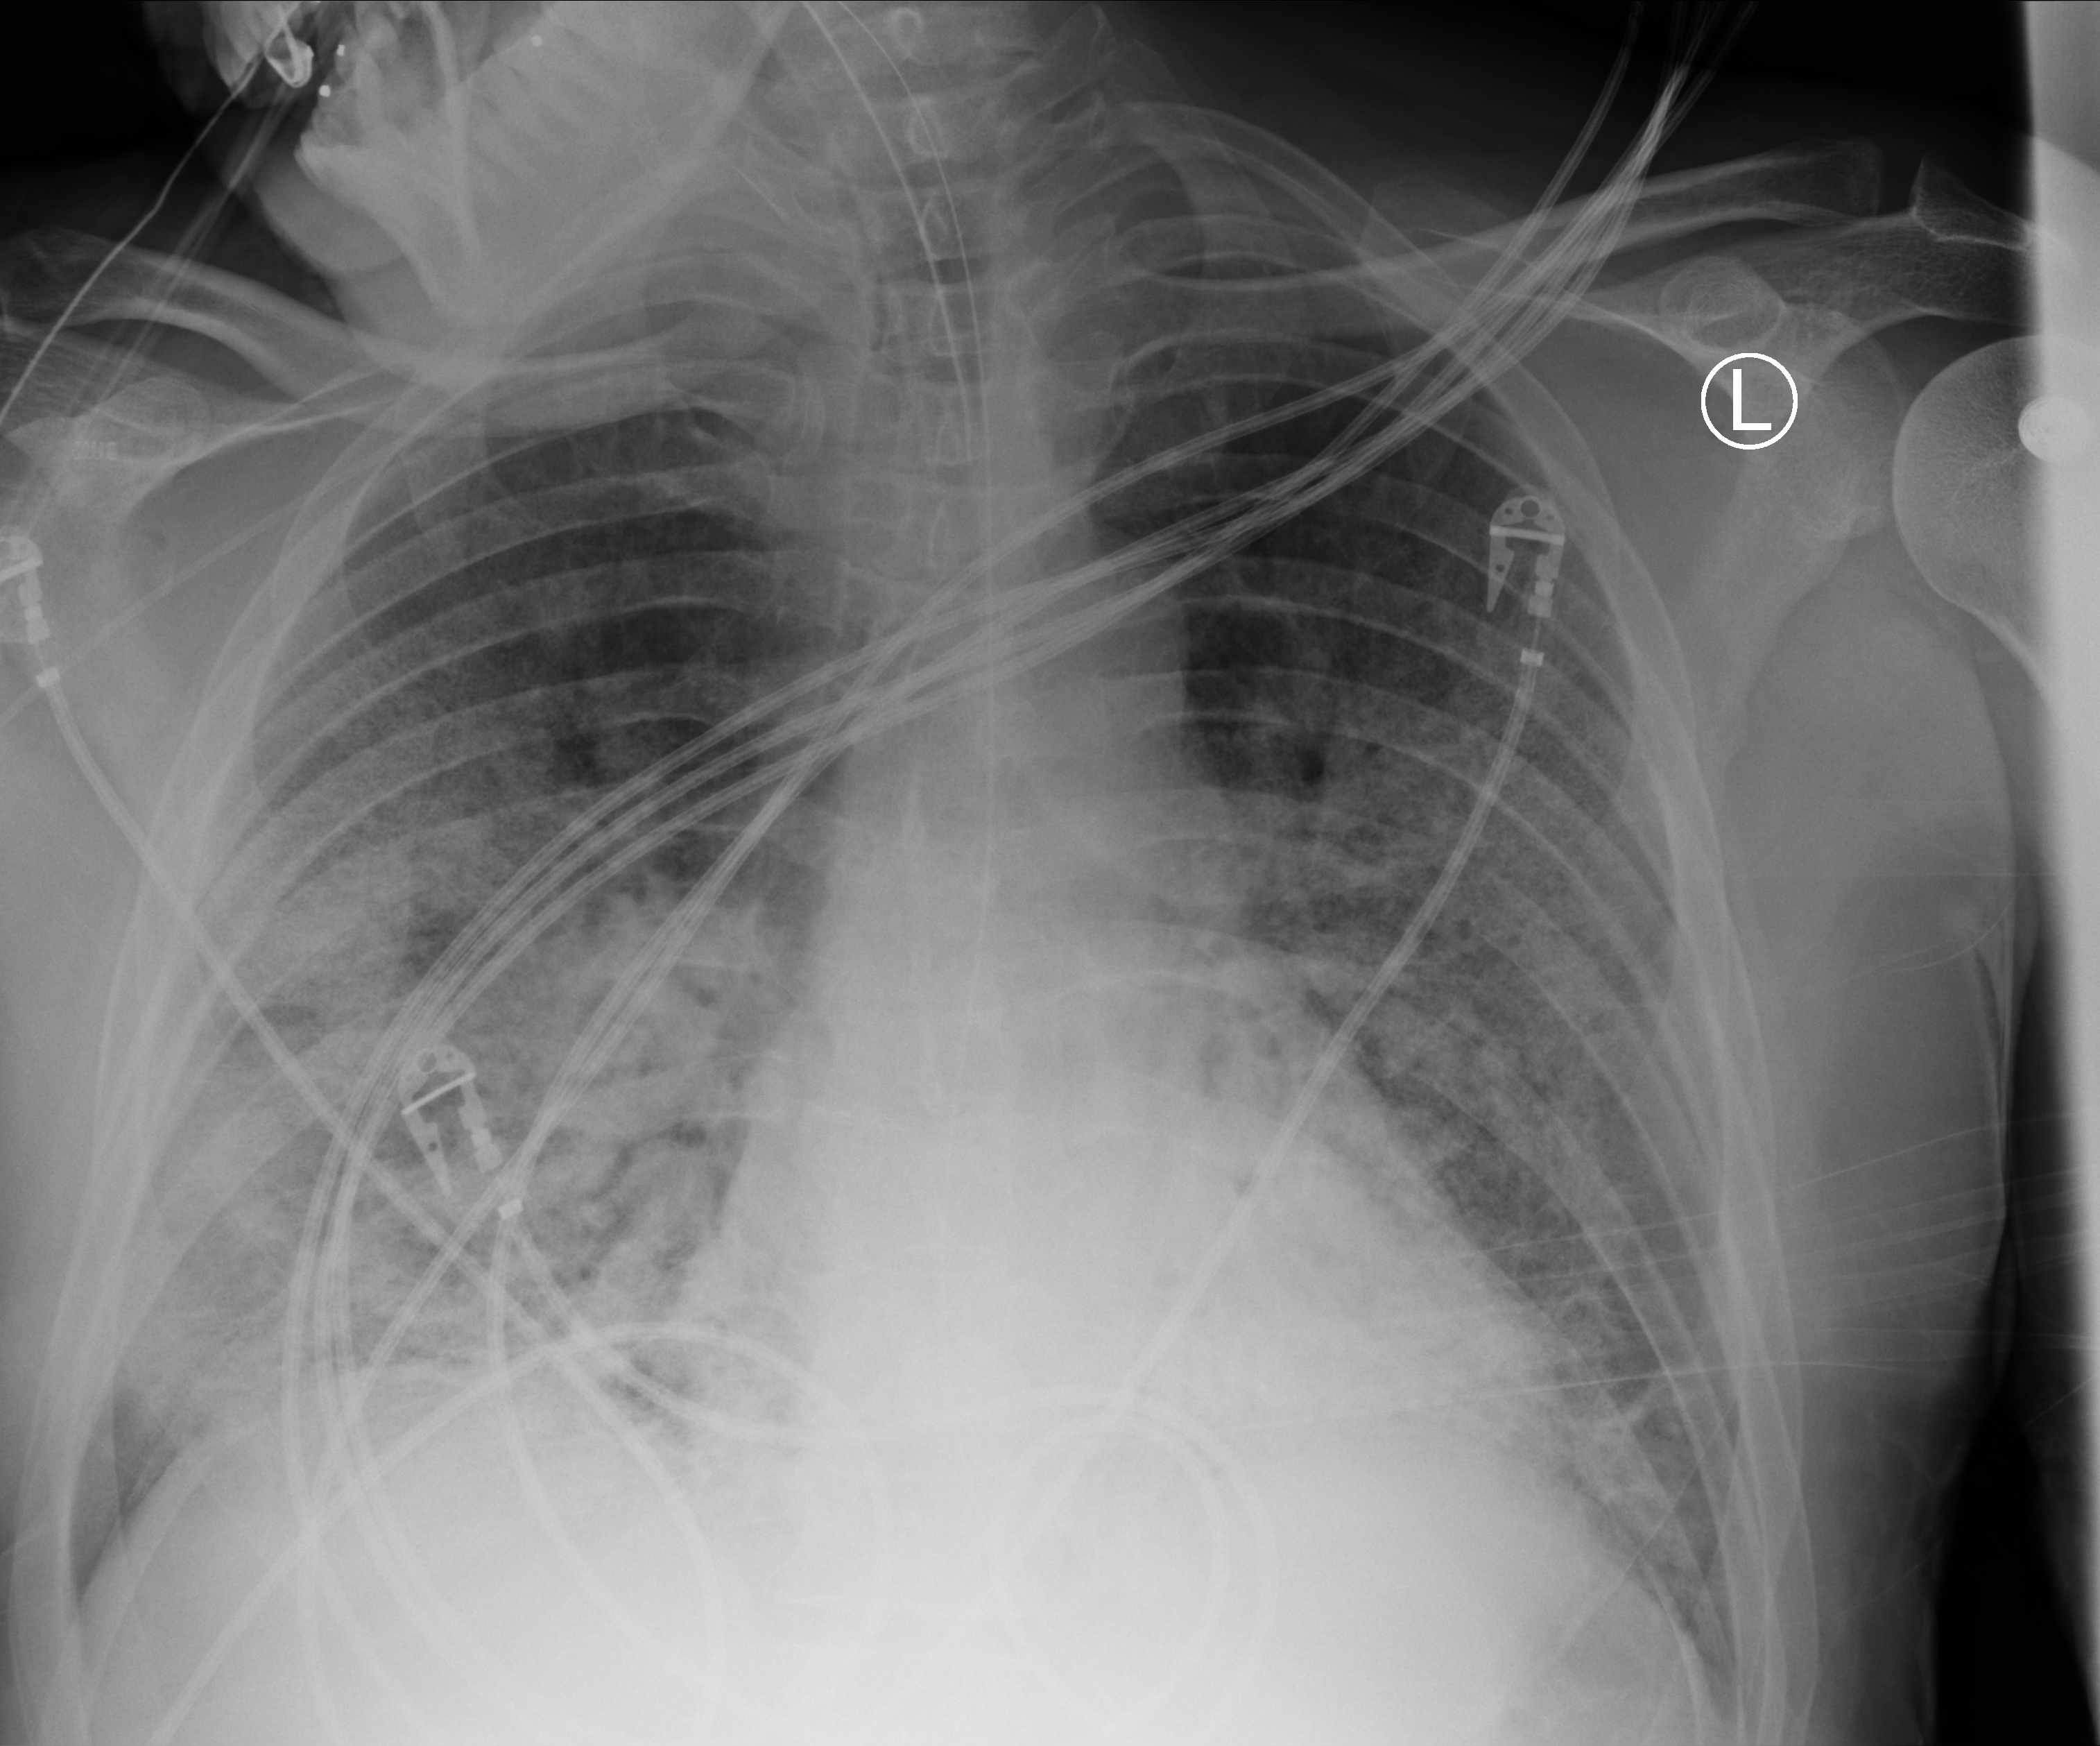
Bedside chest radiograph (computed radiography); anteroposterior (AP) projection. Patient hospitalised with COVID-19; male, aged 18–59 years.
Hospital-stay facts (about this admission, not read from this image; timing relative to this image not recorded): length of hospital stay: 75 days; diabetes (admission record): no; mechanically ventilated during this hospital stay: yes.